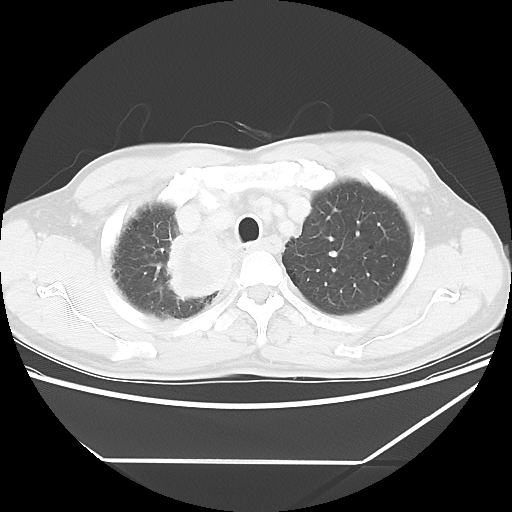
Chest CT, one axial slice; position 50 of 60 along the scan axis; reconstruction kernel LUNG; lung window (W 1500 / L -600 HU); 512 × 512 image matrix, field of view 367 × 367 mm. Patient: male, 58 years. From the clinical record (not read from this slice): clinical TNM (as recorded): T2 N2 M0.
Outlined on this slice (rectangle marked by the reading radiologist):
- lung tumour (recorded histology: squamous cell carcinoma): bounding box (x1, y1, x2, y2) in pixels: (157, 221, 232, 309)